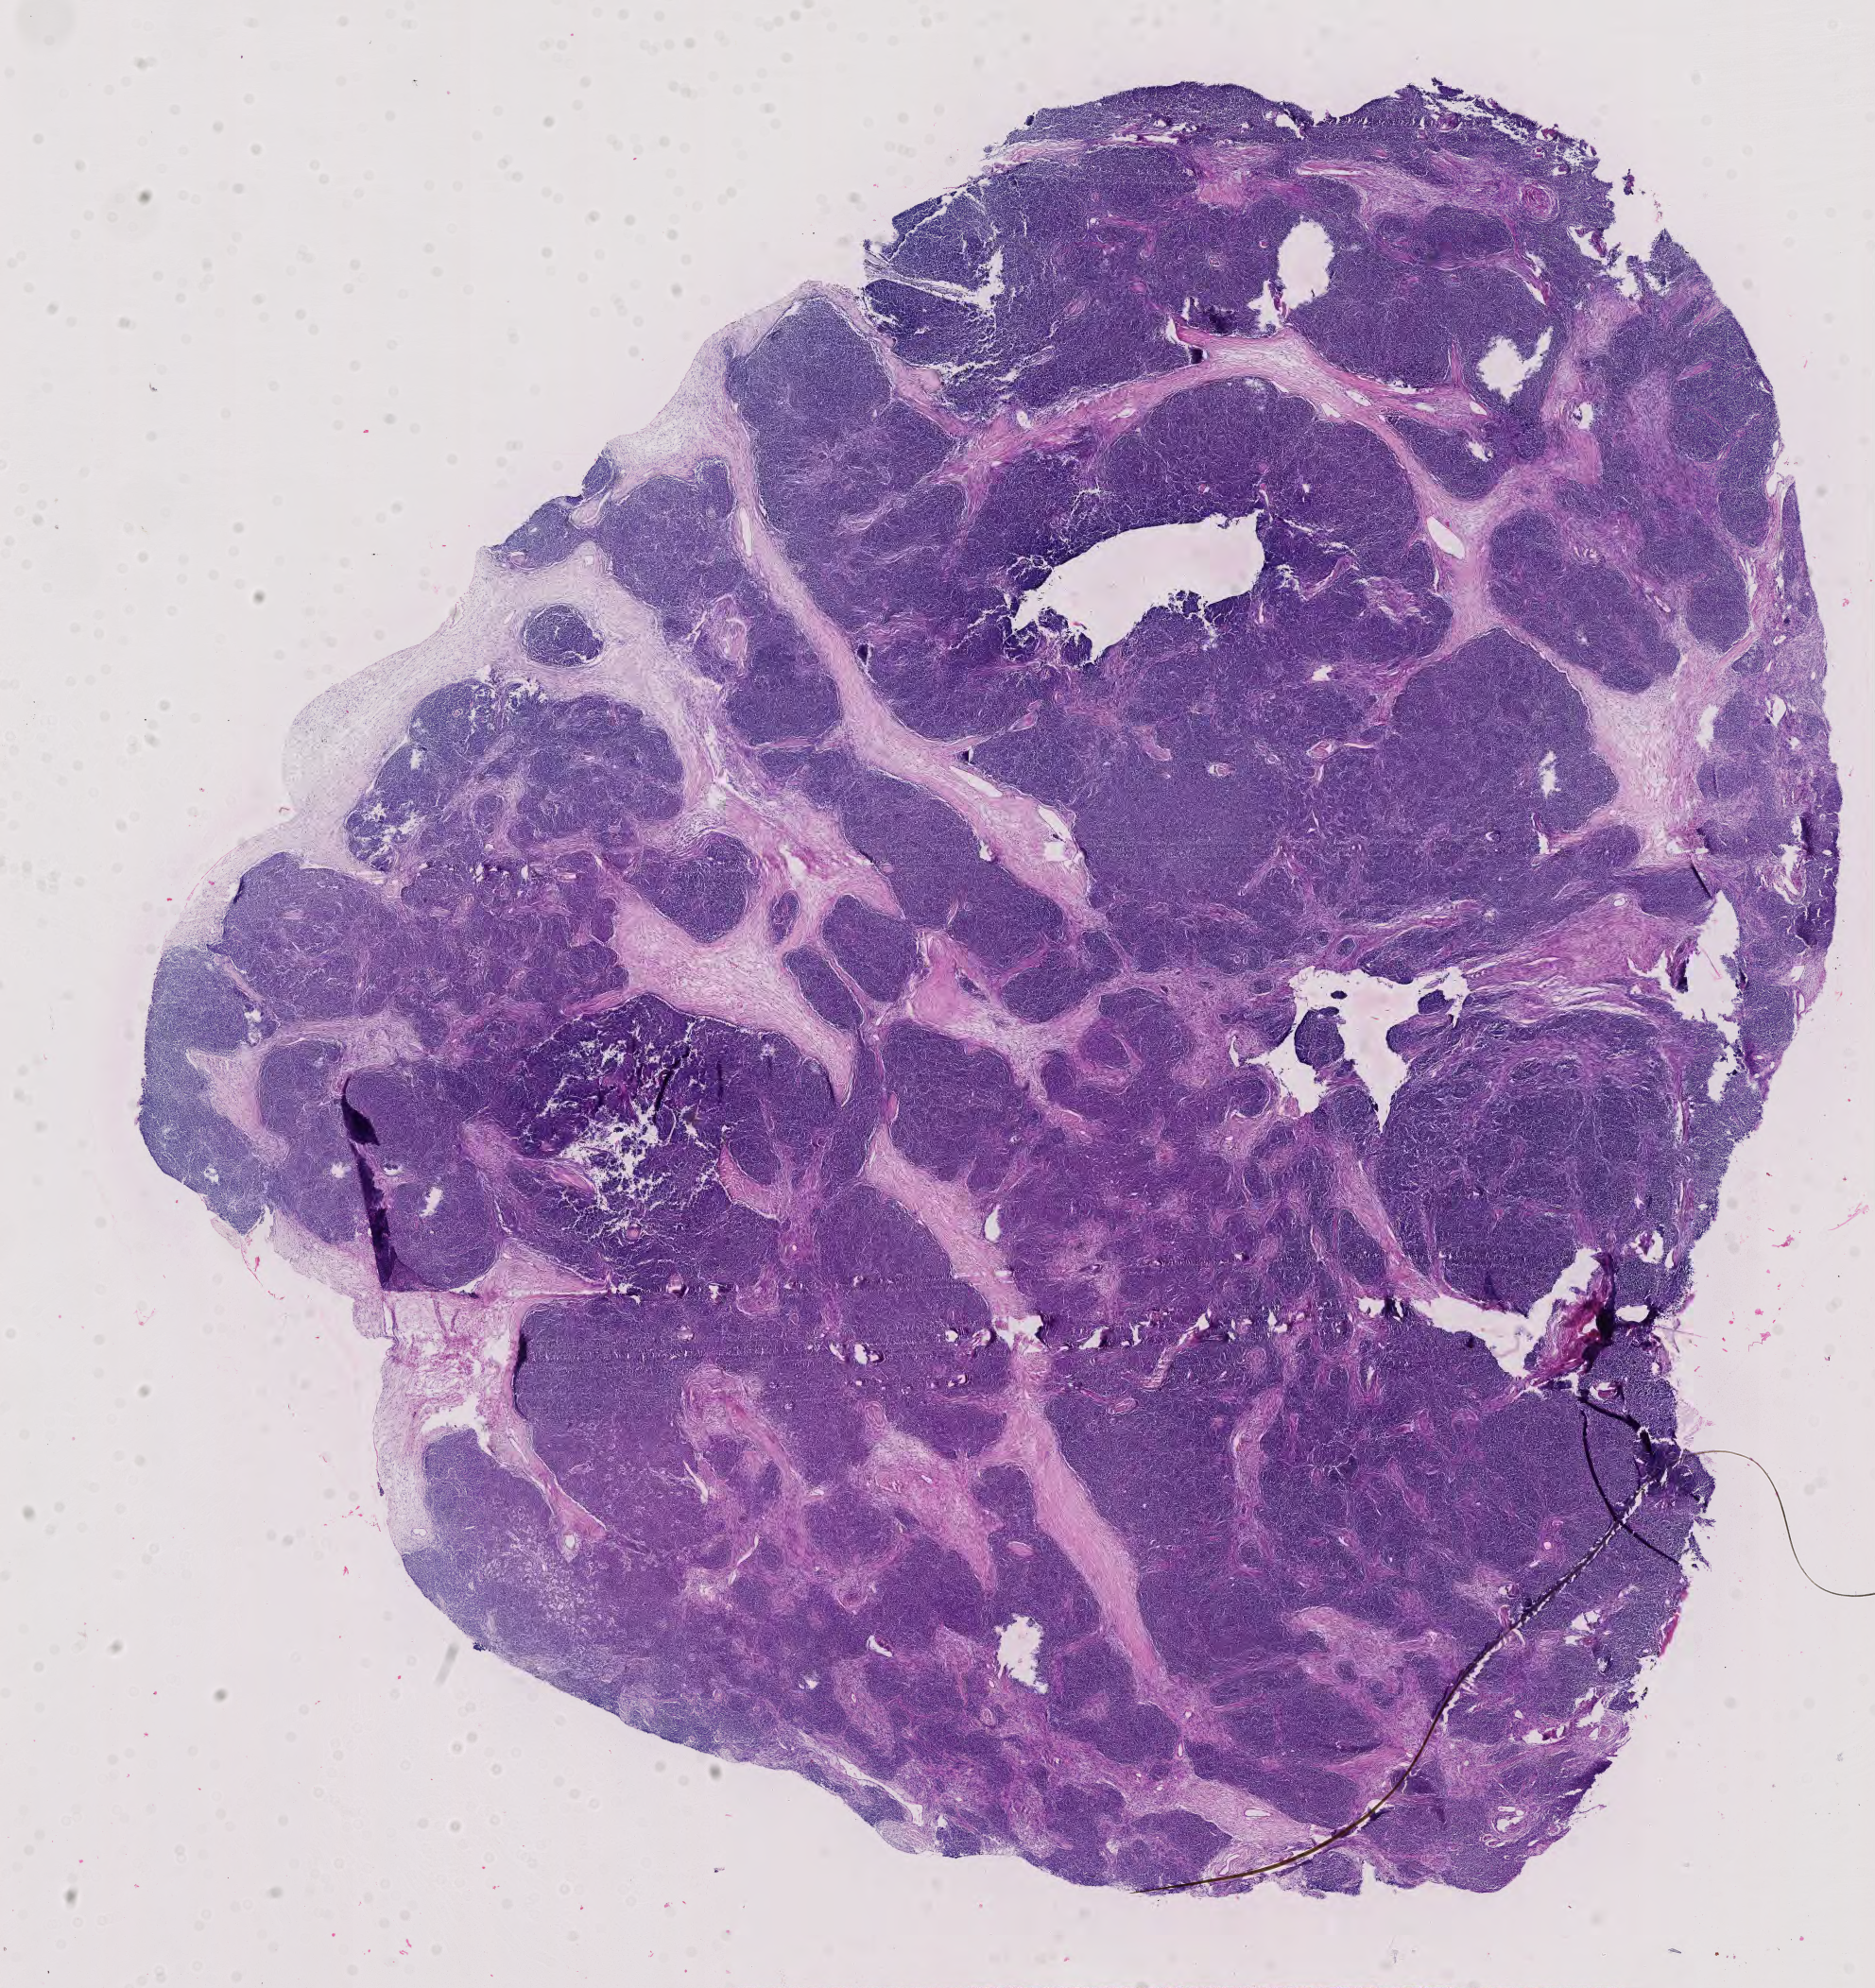
H&E-stained whole-slide image — shown as a low-resolution overview of the whole scanned area (about 14.5 x 15.3 mm); FFPE section; thymus, primary tumour sample. Female, age 77 years at initial diagnosis.
Histologic diagnosis: Thymoma, type AB, malignant.